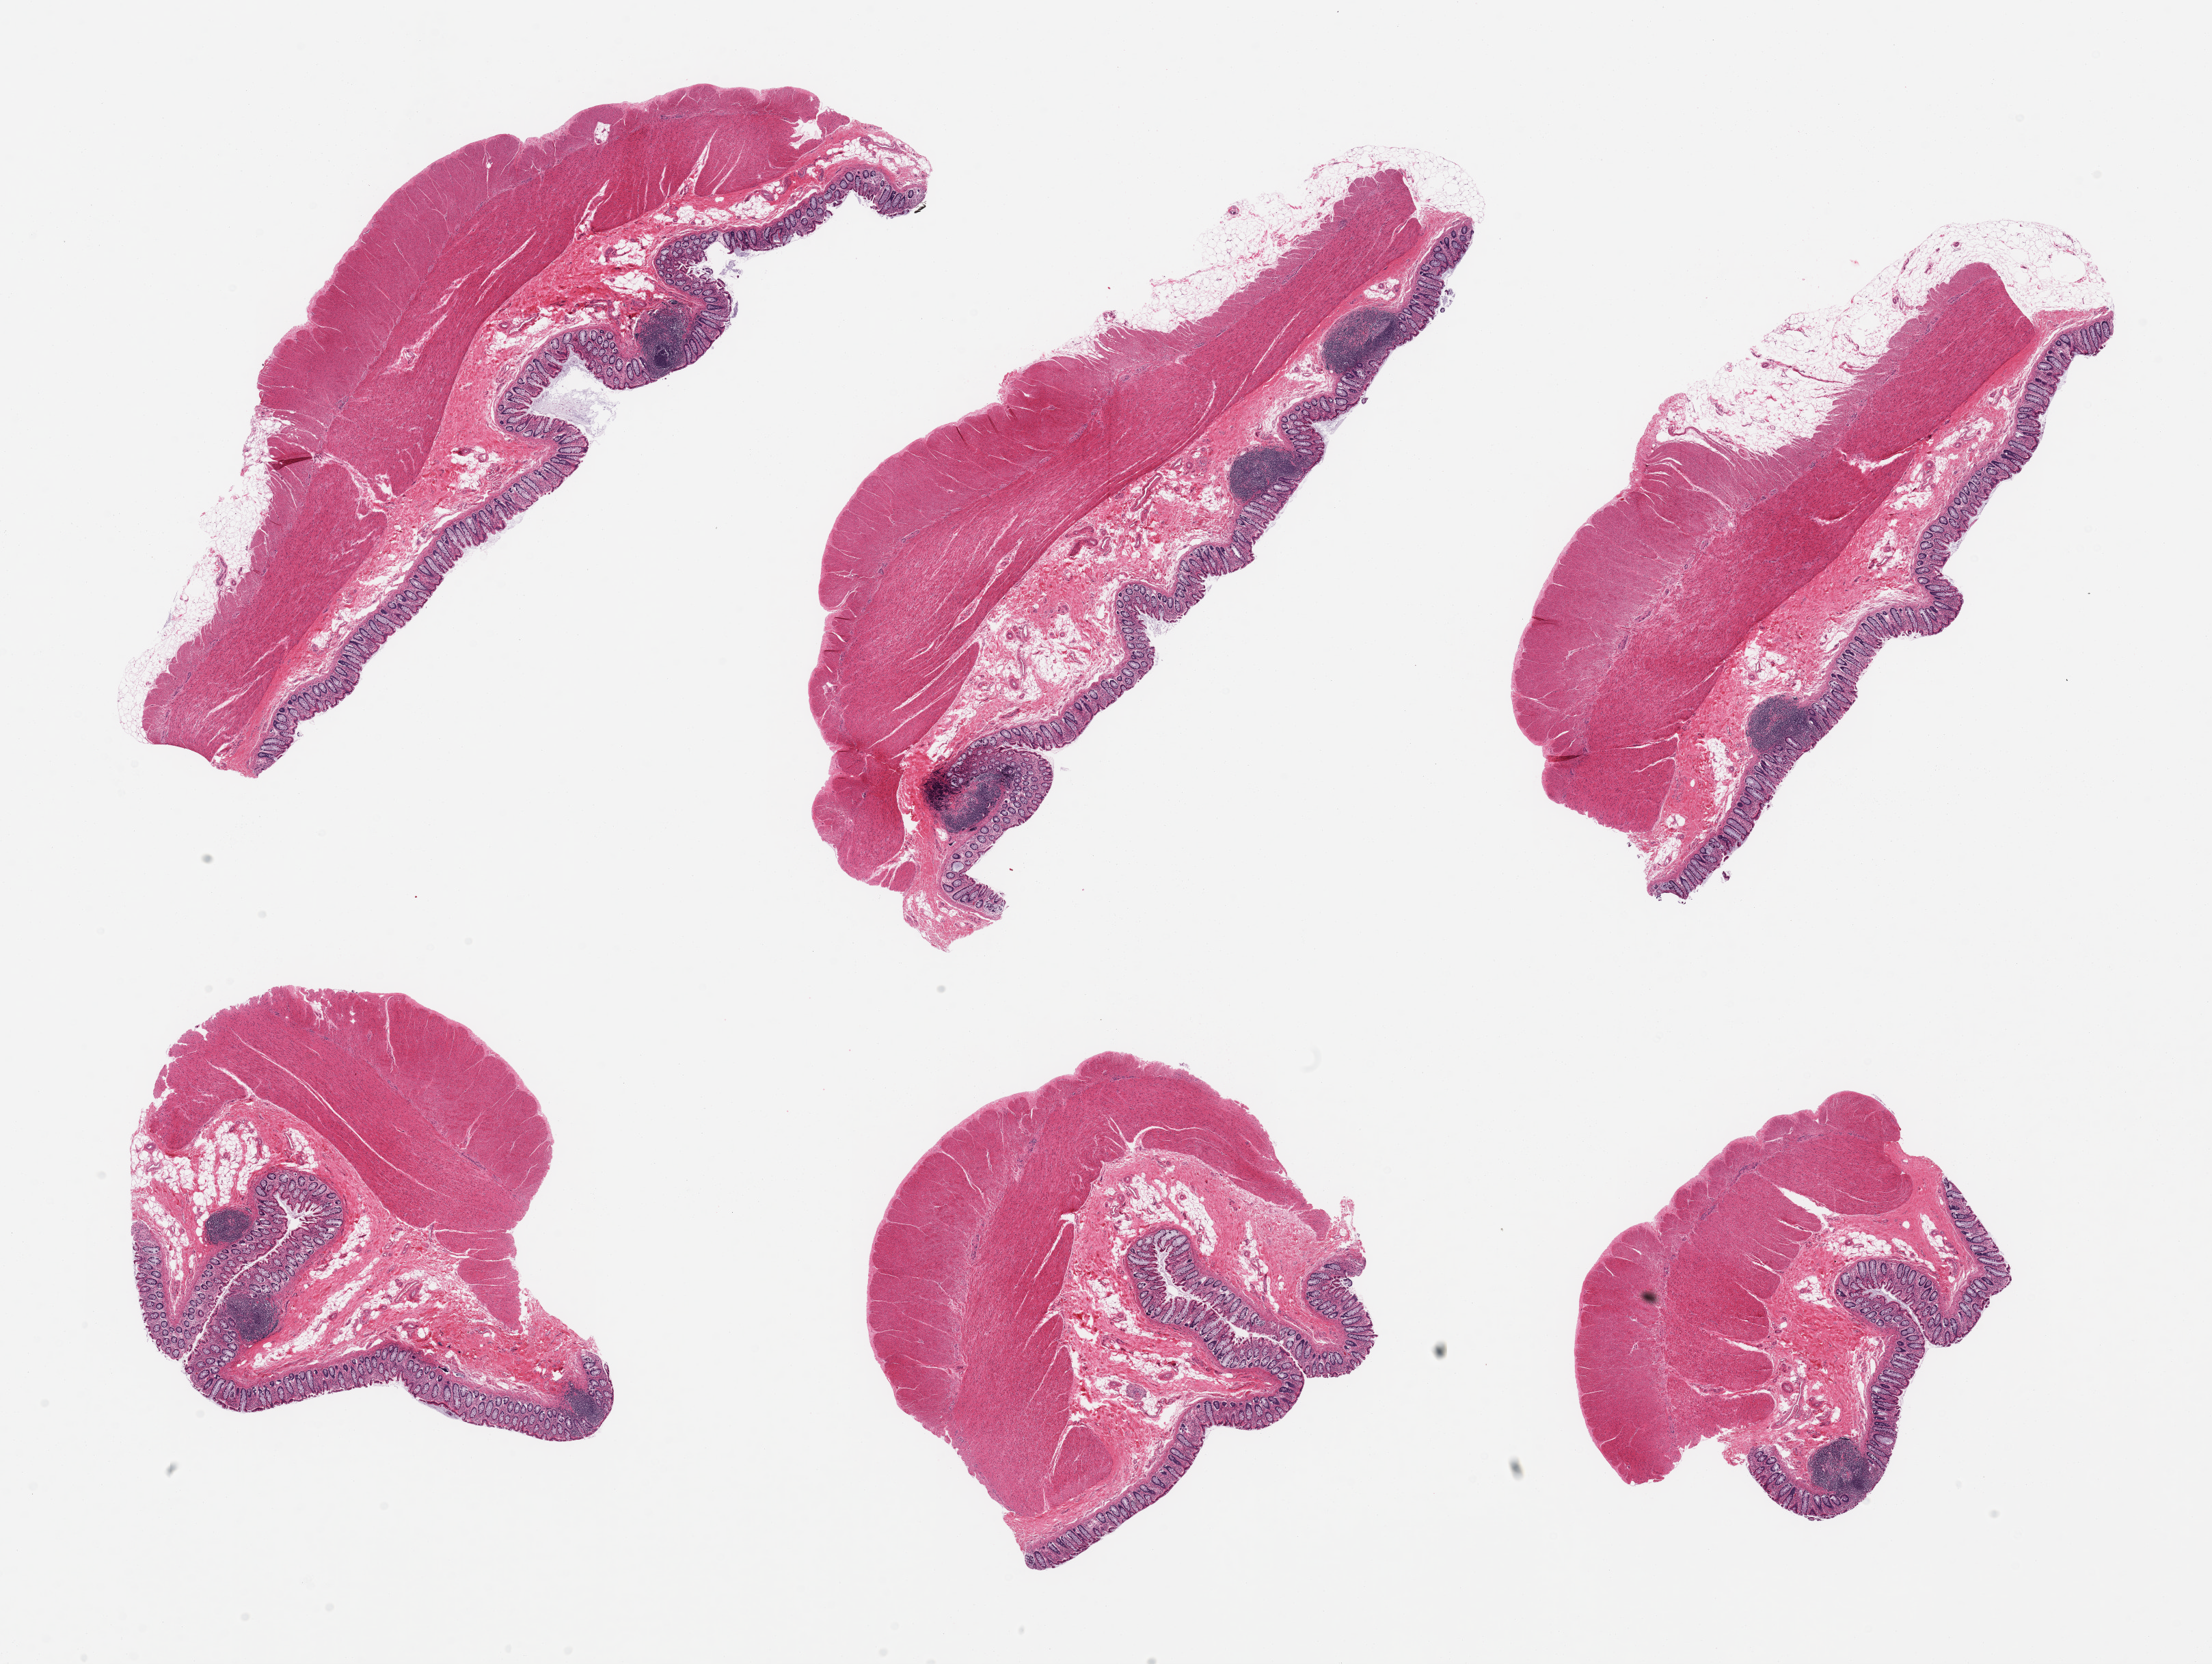
Digitized H&E-stained section, brightfield, a low-resolution overview of the entire scanned area, about 25.6 x 19.3 mm (acquisition: 20x scan); PAXgene-fixed paraffin-embedded (PFPE) section; section of sigmoid colon (target tissue); donor tissue sample. Male donor.
Review note (as recorded): 6 pieces, target muscularis is ~60% of tissue, sample with care.